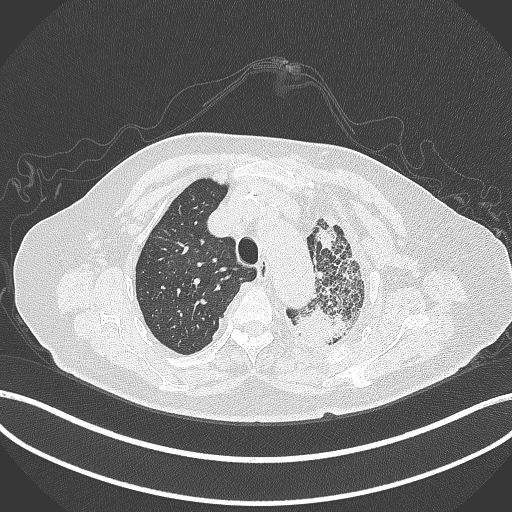
Chest CT, one axial slice. Slice 310 of 399 in the series (ordered by position). Reconstruction kernel B70f. 120 kVp. Lung window (W 1500 / L -600 HU). 1 mm slice thickness. 512 × 512 image matrix, field of view 400 × 400 mm. Patient: female, 75 years. Case-level facts recorded for this patient, not image findings: clinical TNM (as recorded): T3 N3 M1.
Annotated regions visible in this slice (bounding box drawn by a radiologist):
- lung tumour (recorded histology: adenocarcinoma): bounding box (x1, y1, x2, y2) in pixels: (288, 302, 354, 350)